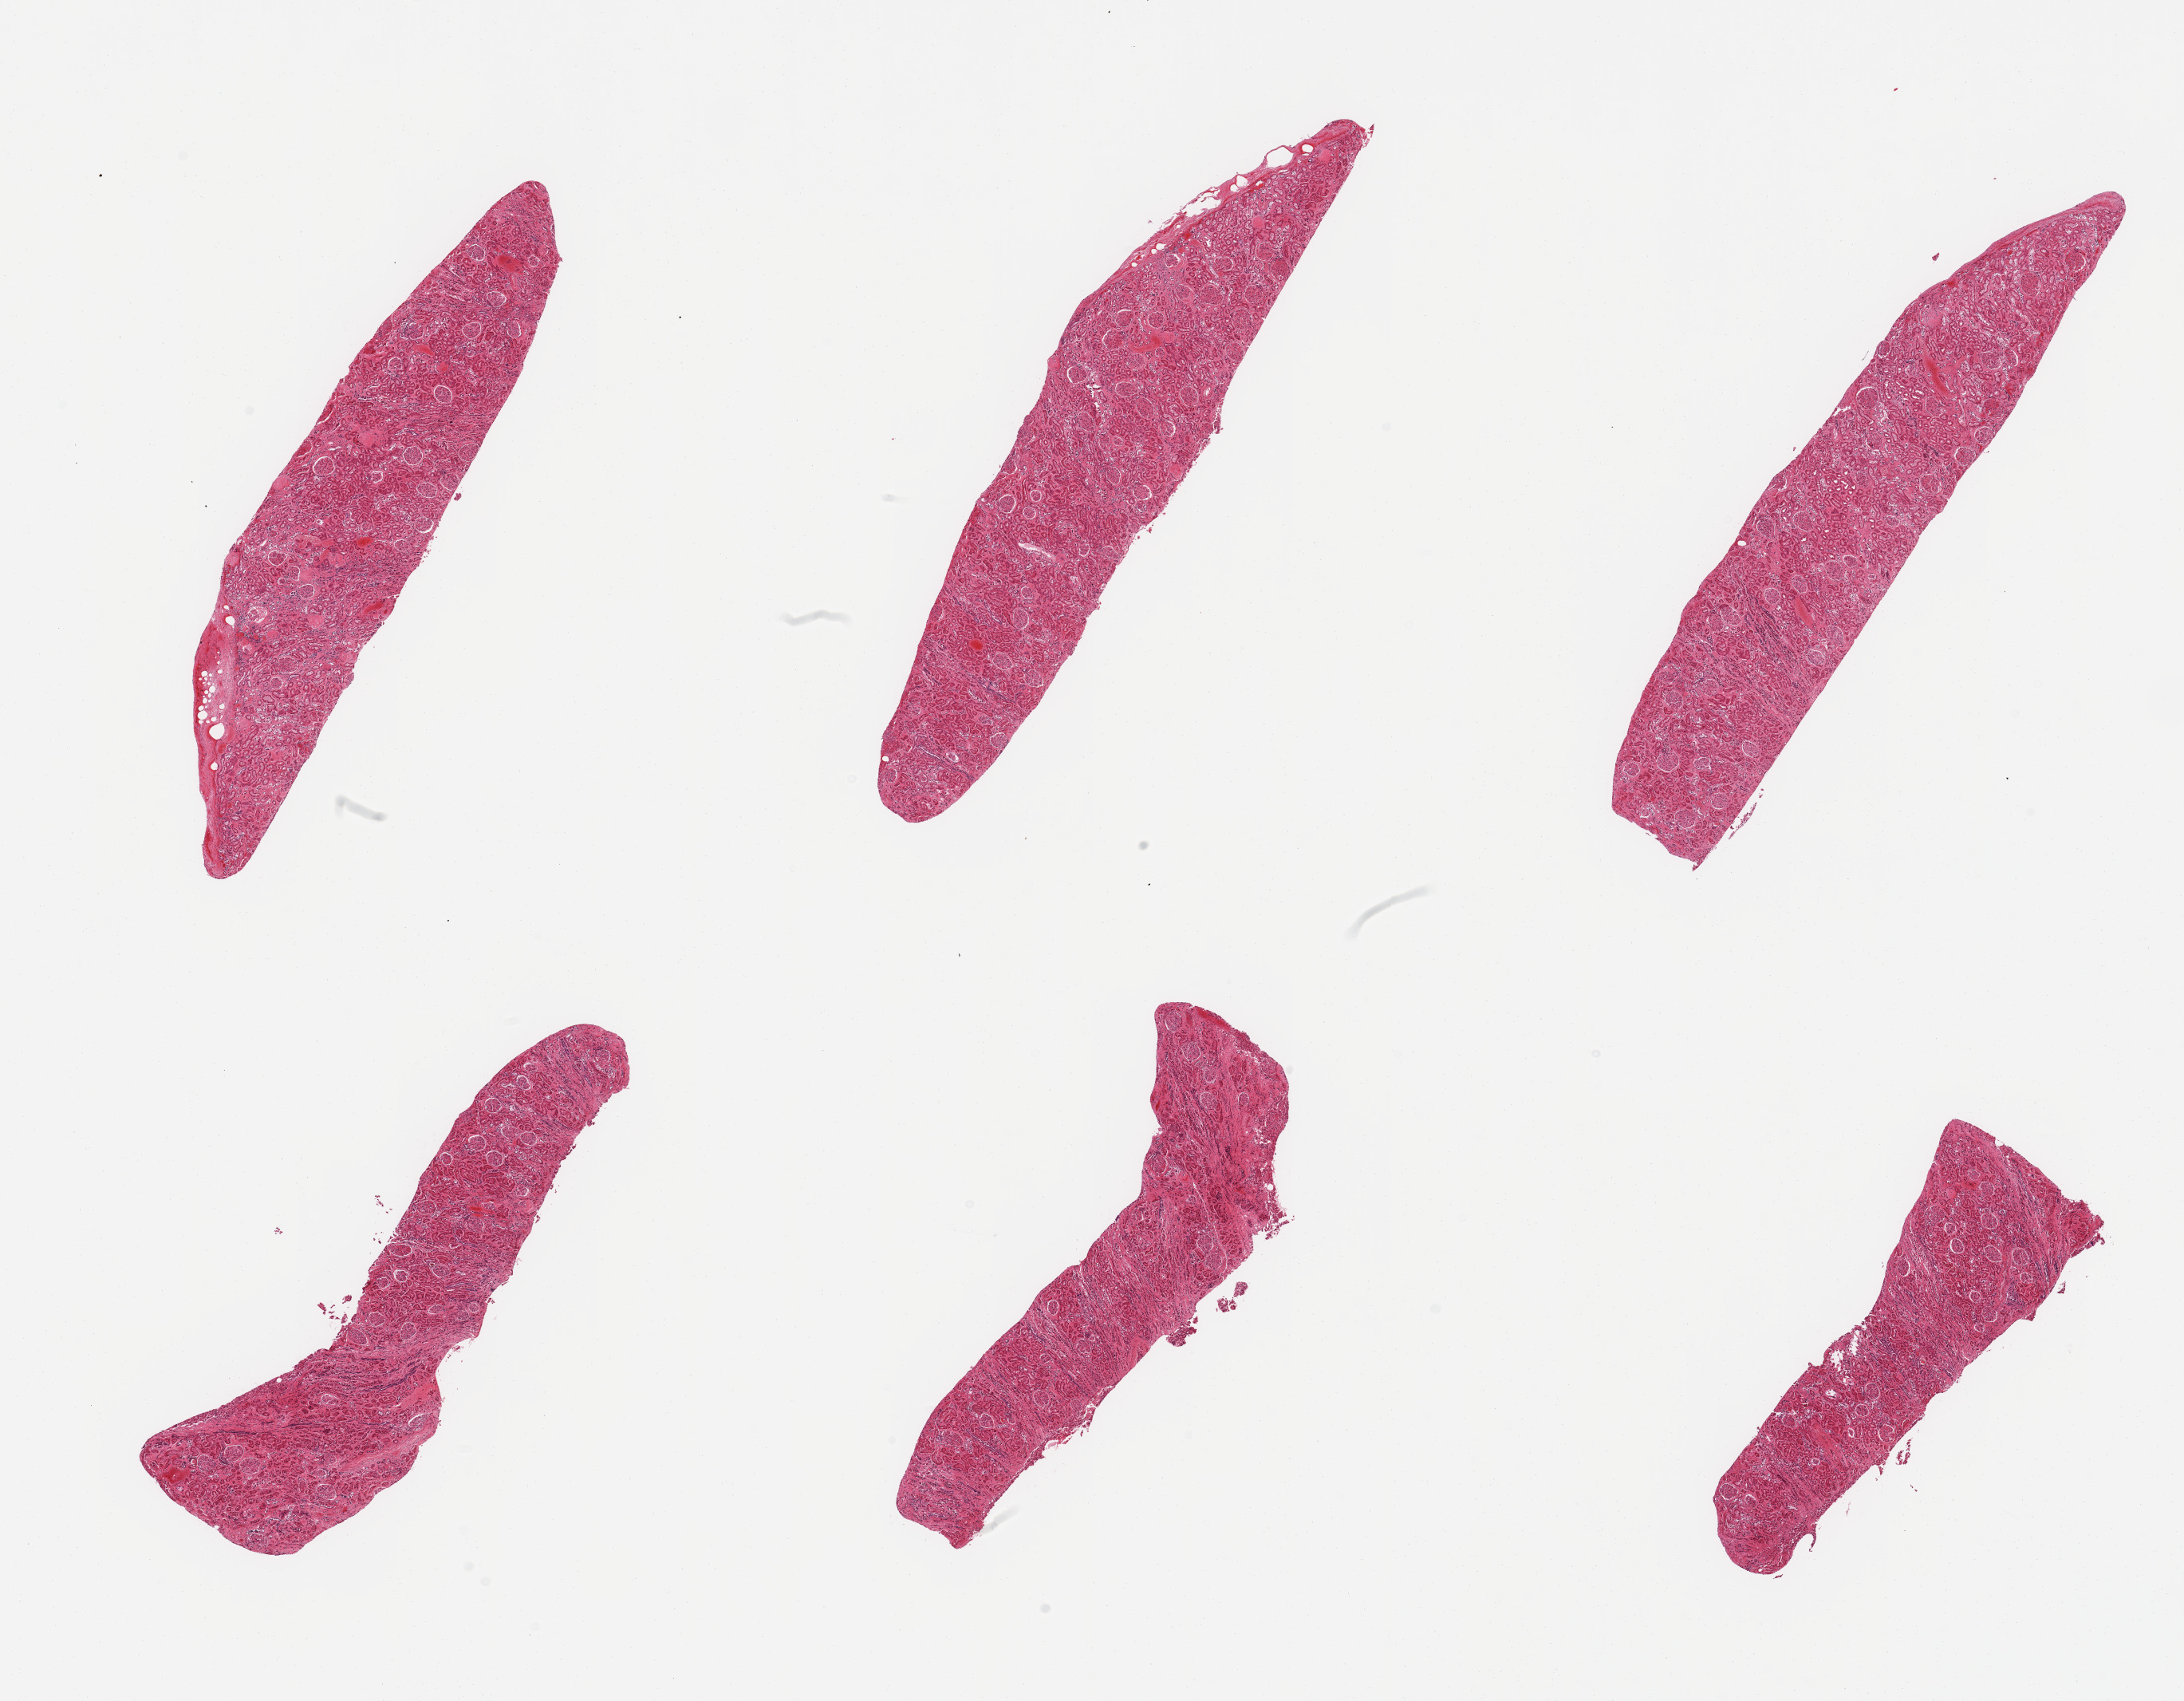
Digitized H&E-stained section, whole scanned area (about 21.7 x 16.9 mm) shown as a low-resolution overview; PAXgene-fixed, paraffin-embedded tissue; section of renal cortex (target tissue); tissue donor sample.
Reviewer comment on this tissue sample: 6 pieces, glomeruli present; tubules moderately autolyzed.